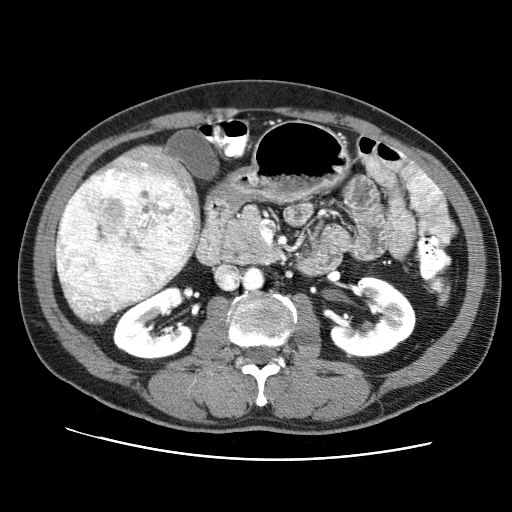
Contrast-enhanced abdominal CT (liver protocol), one axial slice; slice 28 of 71 in the series (ordered by position); reconstruction kernel STANDARD; soft-tissue window (W 400 / L 40 HU); 2.5 mm slice thickness; 512 × 512 image matrix, field of view 360 × 360 mm. Case-level facts recorded for this patient, not image findings: diagnosis: hepatocellular carcinoma (patient treated with transarterial chemoembolisation; whether this scan precedes or follows treatment is not stated here); TNM stage (as recorded): Stage-II; Child-Pugh class: A; tumour nodularity: multinodular.
Outlined on this slice (semi-automatic segmentation, software-assisted and operator-edited):
- liver parenchyma outside the tumour (the mass and vessels are separate outlines, so this box may not span the whole liver): bounding box [x1, y1, x2, y2] px = [64, 148, 200, 300]
- mass: [55, 171, 193, 324]
- liver vessels: [106, 158, 195, 225]